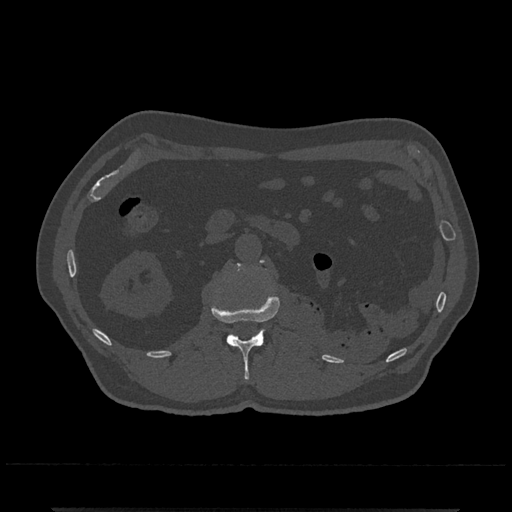
CT including the spine, one axial slice. Position 343 of 797 along the scan axis. Bone window (W 1800 / L 400 HU). 0.5 mm slice thickness. 512 × 512 image matrix, field of view 393 × 393 mm. Patient: male, 67 years. From the clinical record (not read from this slice): primary cancer: prostate.
Annotated regions visible in this slice (semi-automatically segmented with operator editing):
- L1 vertebra: bounding box <212,295,280,380> (left, top, right, bottom; pixels)
- L2 vertebra: <236,260,265,271>